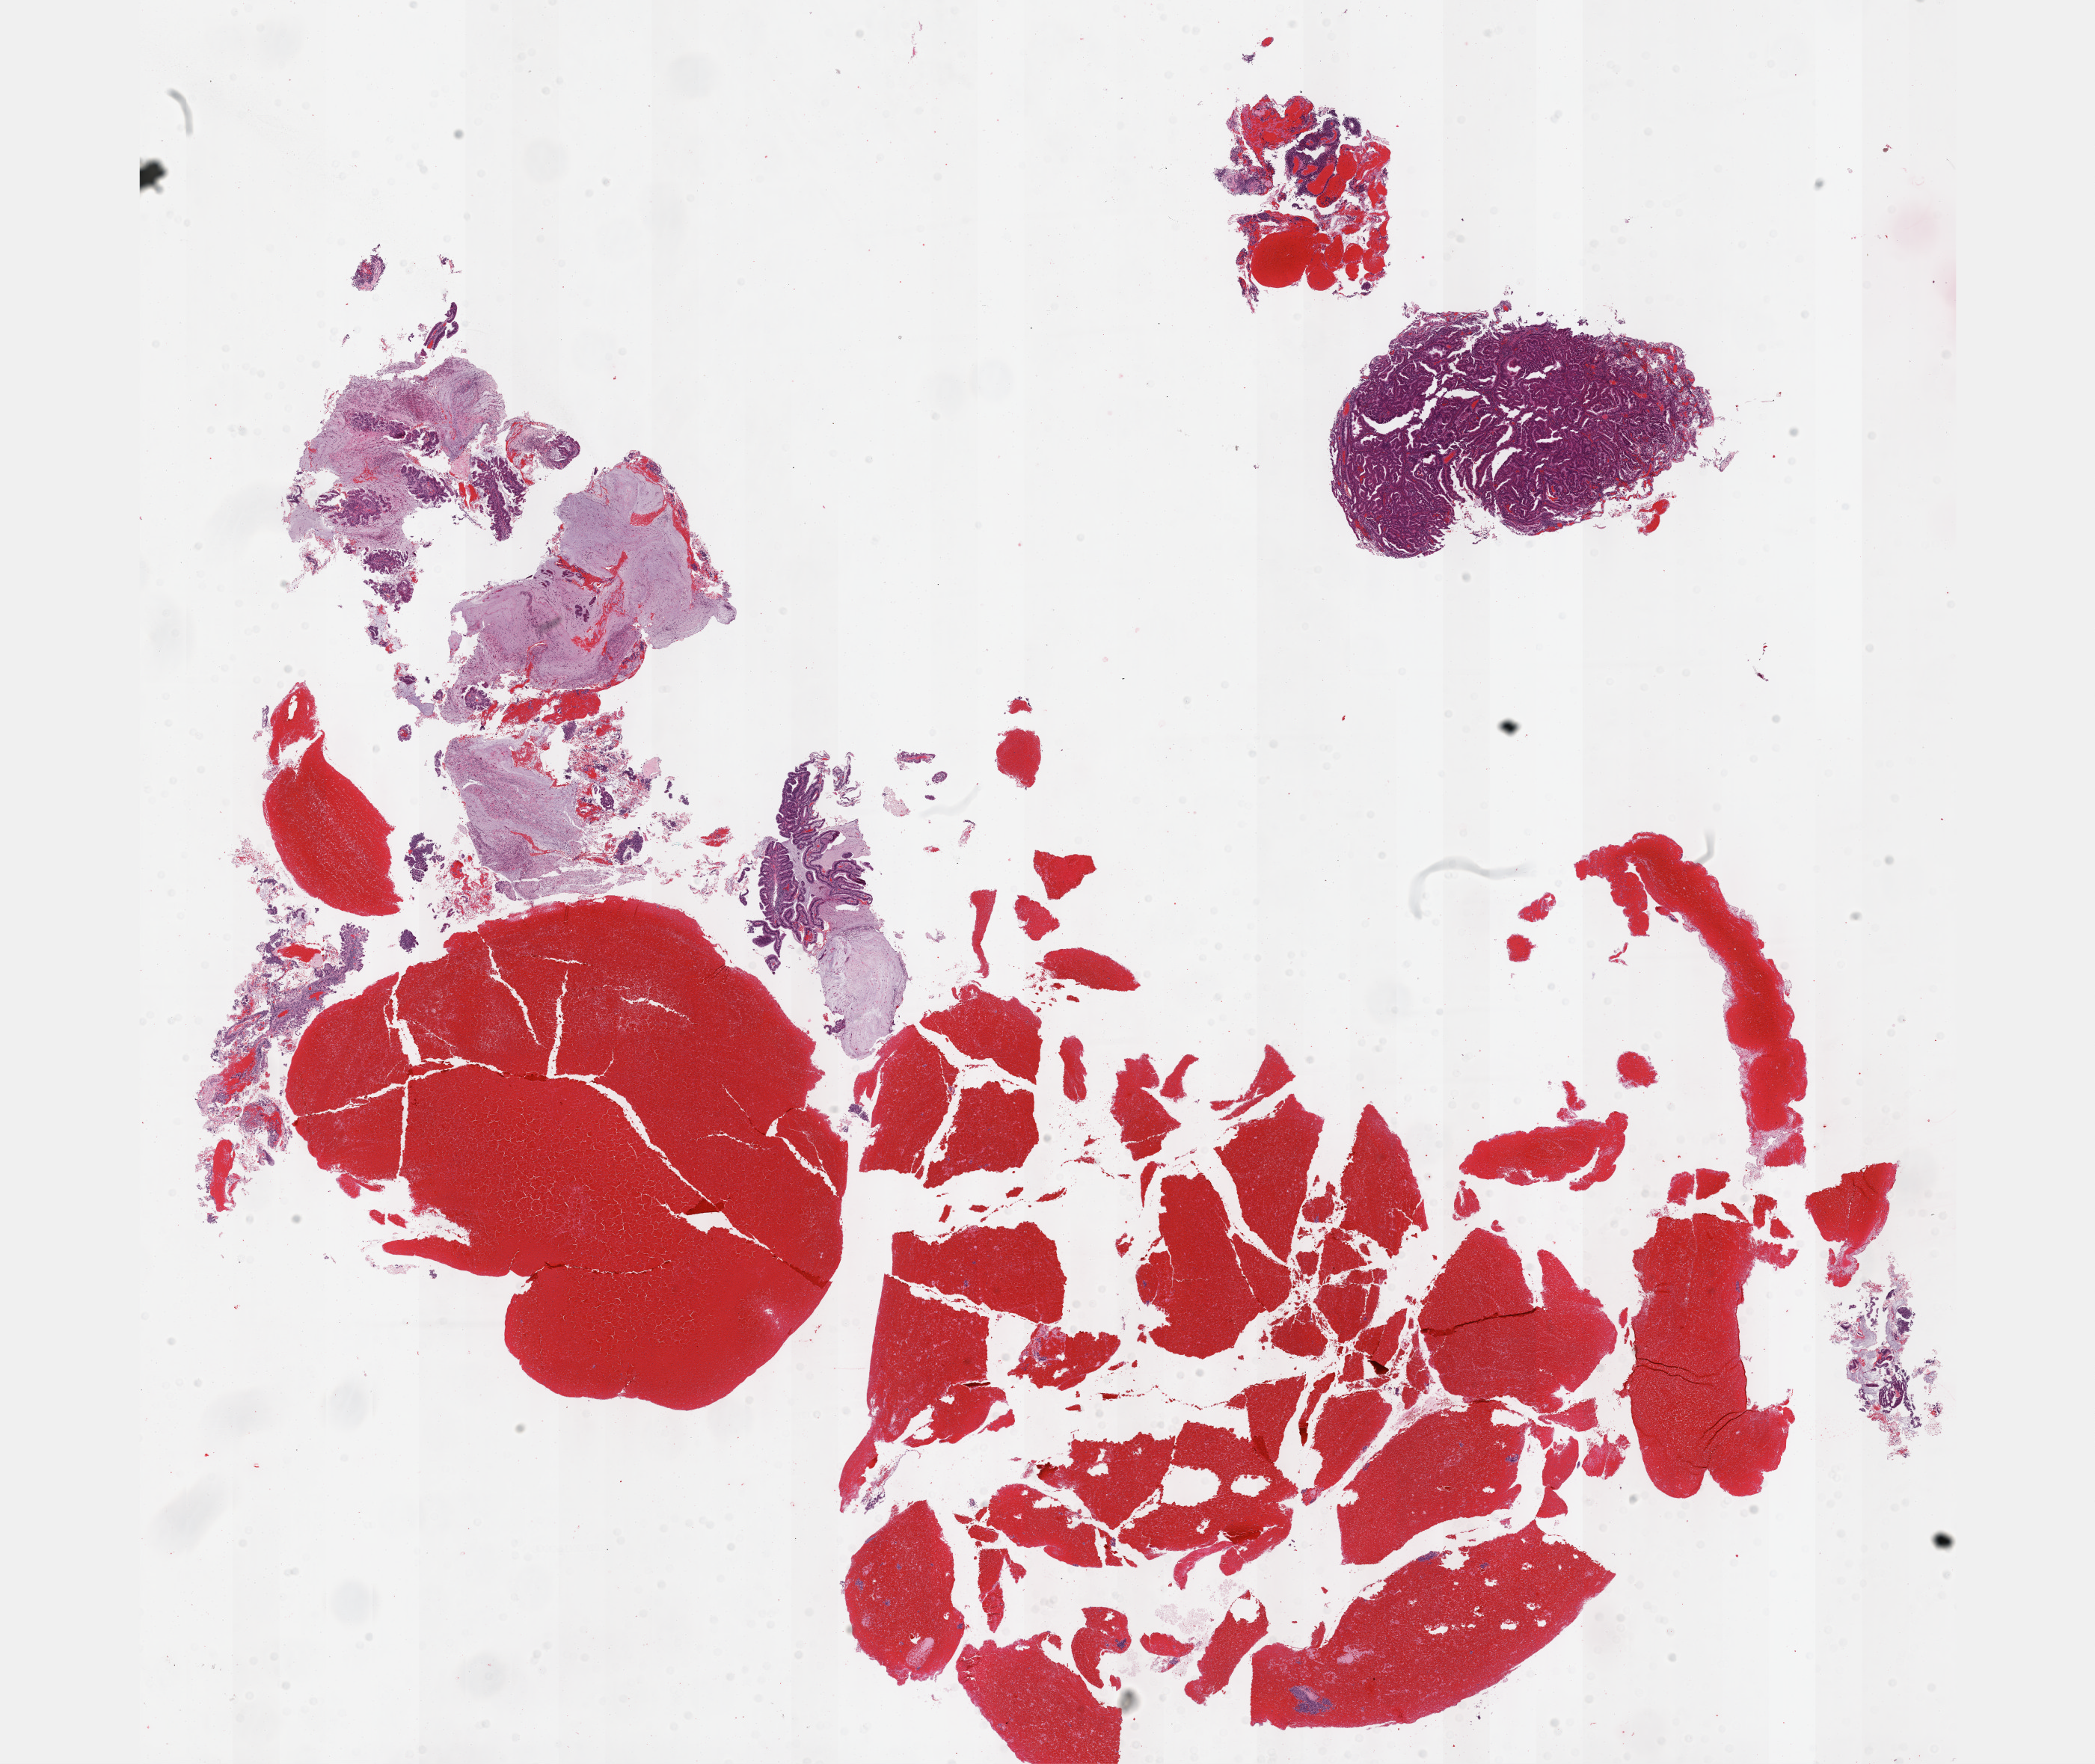
Digitized H&E-stained tissue section (whole slide) — low-resolution overview of the scanned area, about 22.6 x 19.1 mm (slide scanned at 40x), formalin-fixed paraffin-embedded (FFPE) diagnostic section, sample: primary tumour, cervix. Female patient; age at initial diagnosis 45 years. Histologic grade: GX (grade cannot be assessed).
Diagnosis: Adenocarcinoma, endocervical type (cervix uteri). FIGO stage: I.